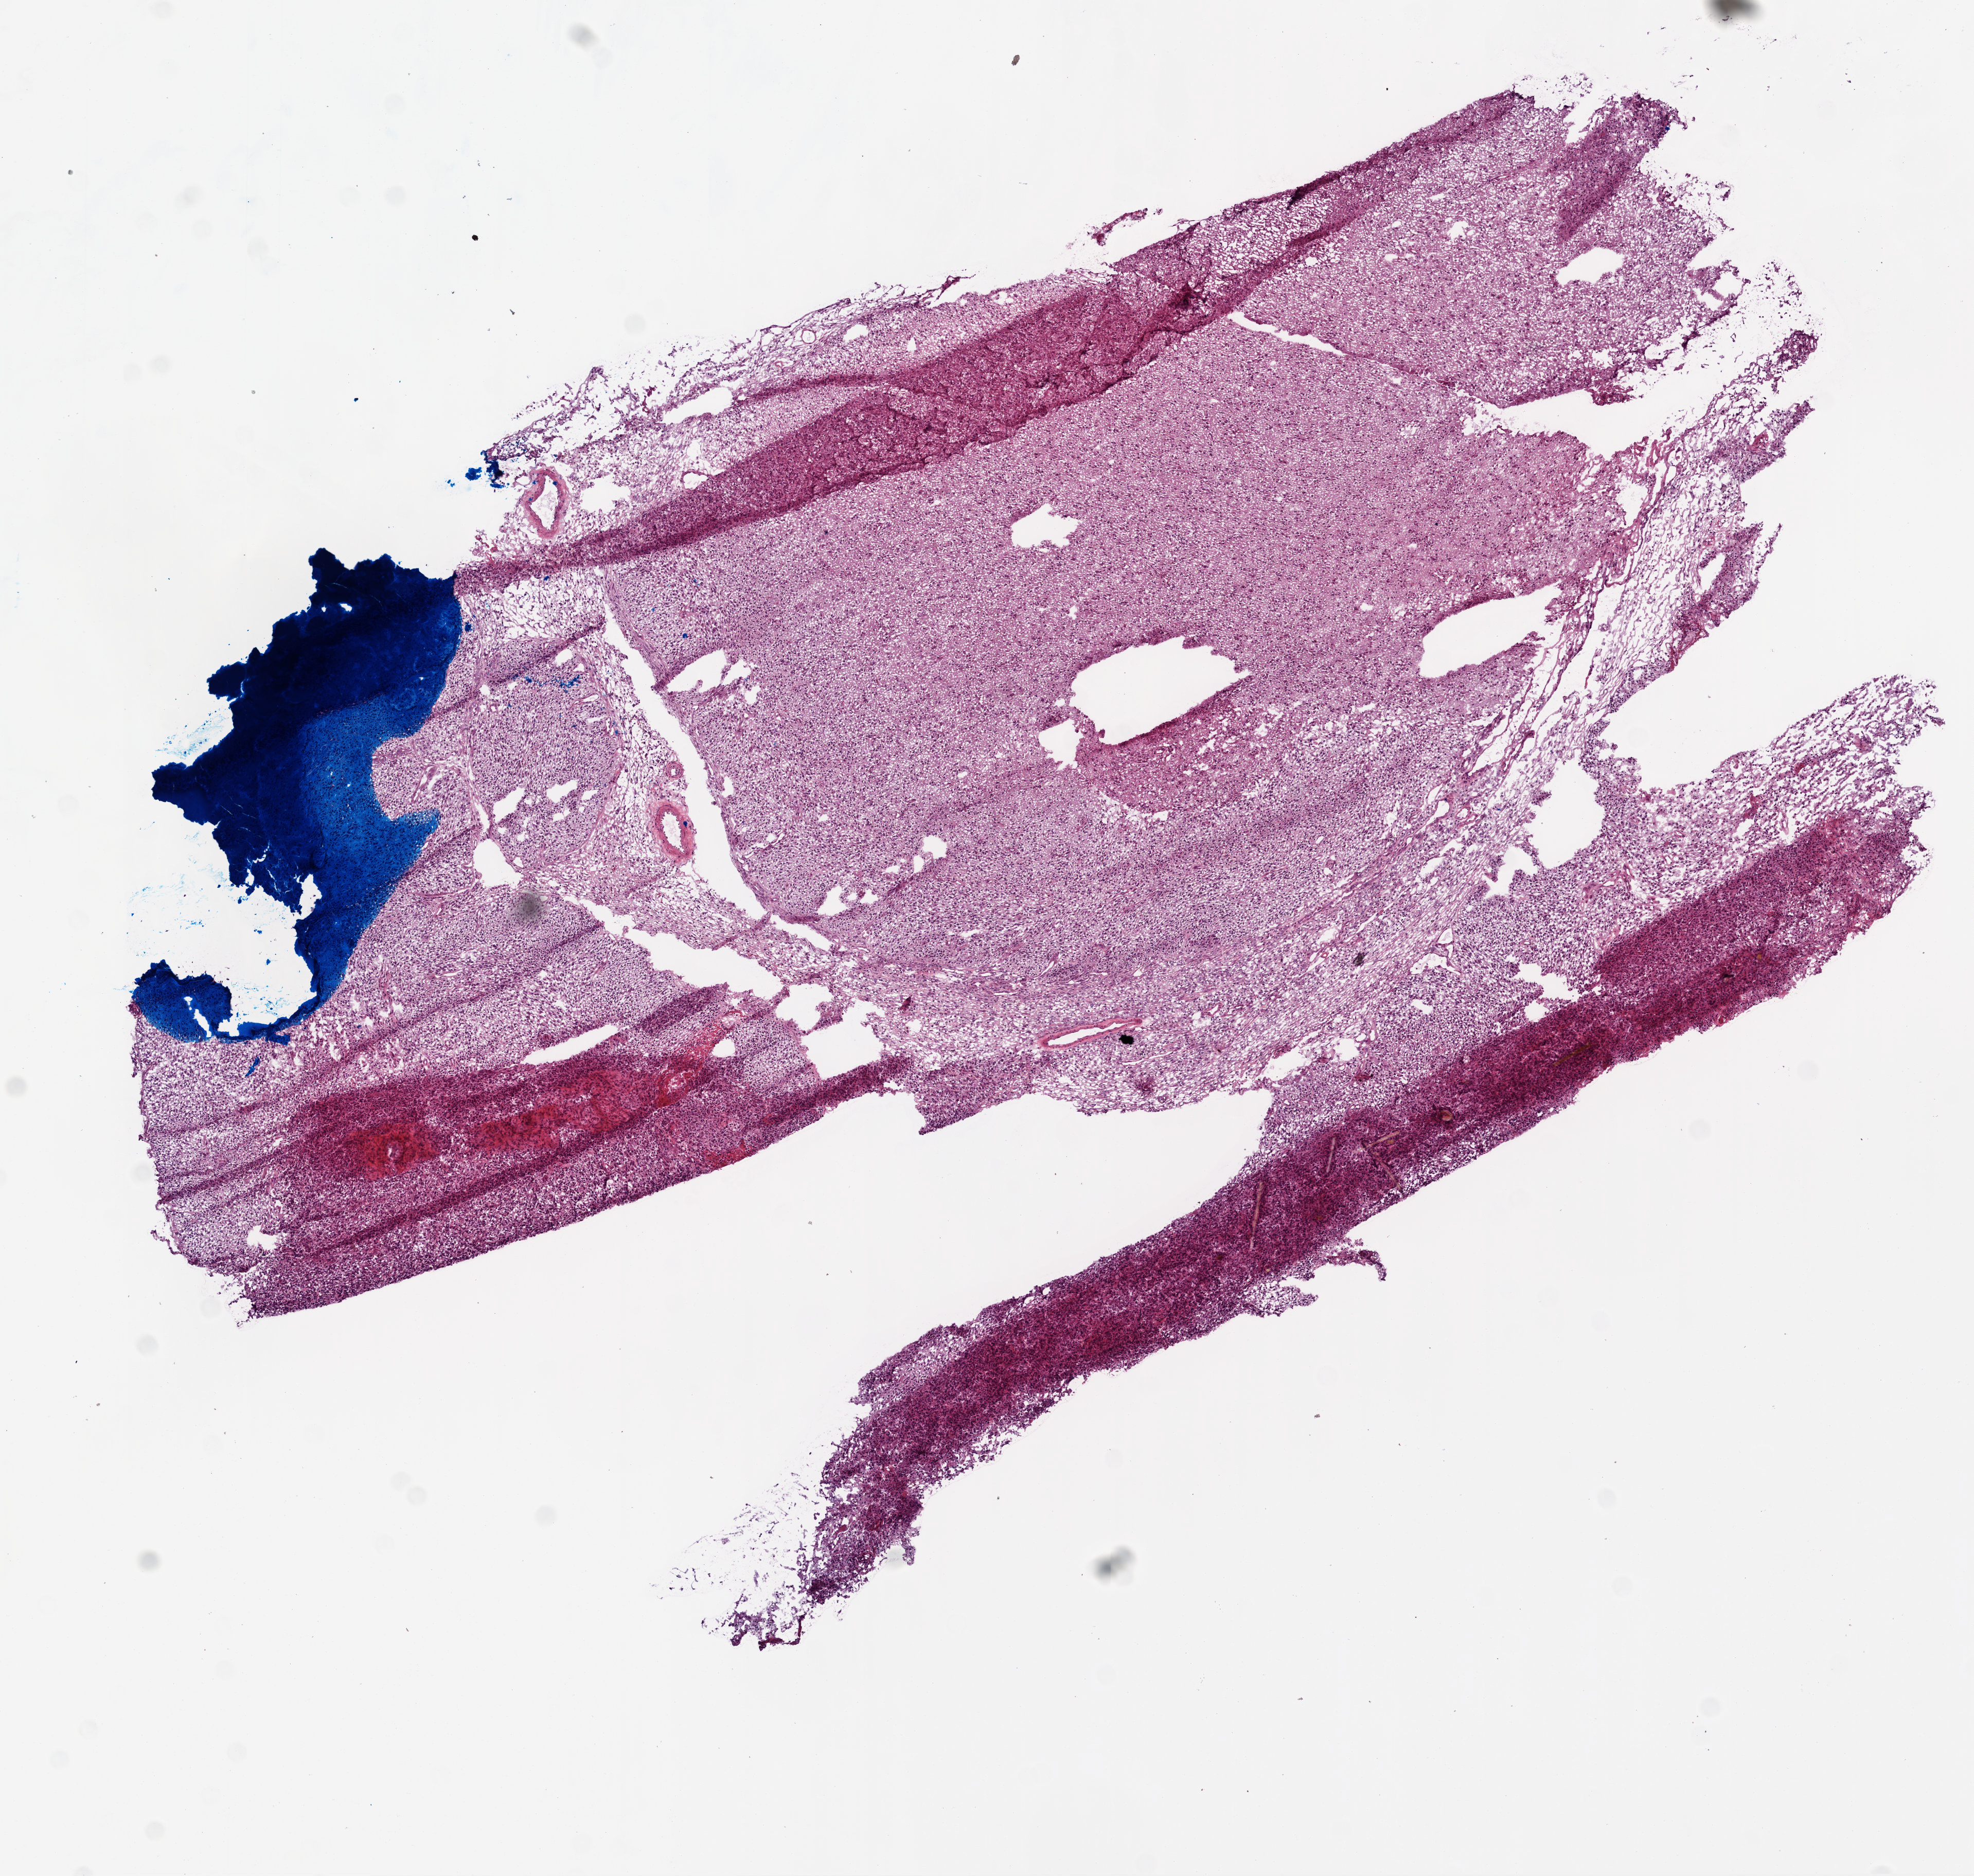
Whole-slide histology image, H&E, shown as a low-resolution overview of the whole scanned area (about 7.7 x 7.4 mm). Frozen section. Sample: primary tumour, brain. Male patient; age at initial diagnosis 69 years. Slide review estimates, as recorded: tumour cells 70%, tumour nuclei 95%, normal cells 0%, stromal cells 25%, necrosis 5%.
- diagnosis: Glioblastoma